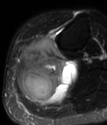
MRI of an extremity soft-tissue mass, one axial slice. Slice 35 of 78 in the series (ordered by position). T2-weighted fat-saturated. MR volume resampled by the dataset authors to the PET/CT grid (not the native acquisition matrix). 107 × 125 image matrix, field of view 104 × 122 mm. Female patient. Case-level facts recorded for this patient, not image findings: histological type: extraskeletal high grade osteogenic sarcoma; grade: high; site of the primary tumour: left calf.
Structures marked on this image (expert contour drawn on MRI and transferred to this co-registered scan by the dataset authors):
- gross tumour volume (mass): bounding box (x1, y1, x2, y2) in pixels: (17, 38, 77, 105)